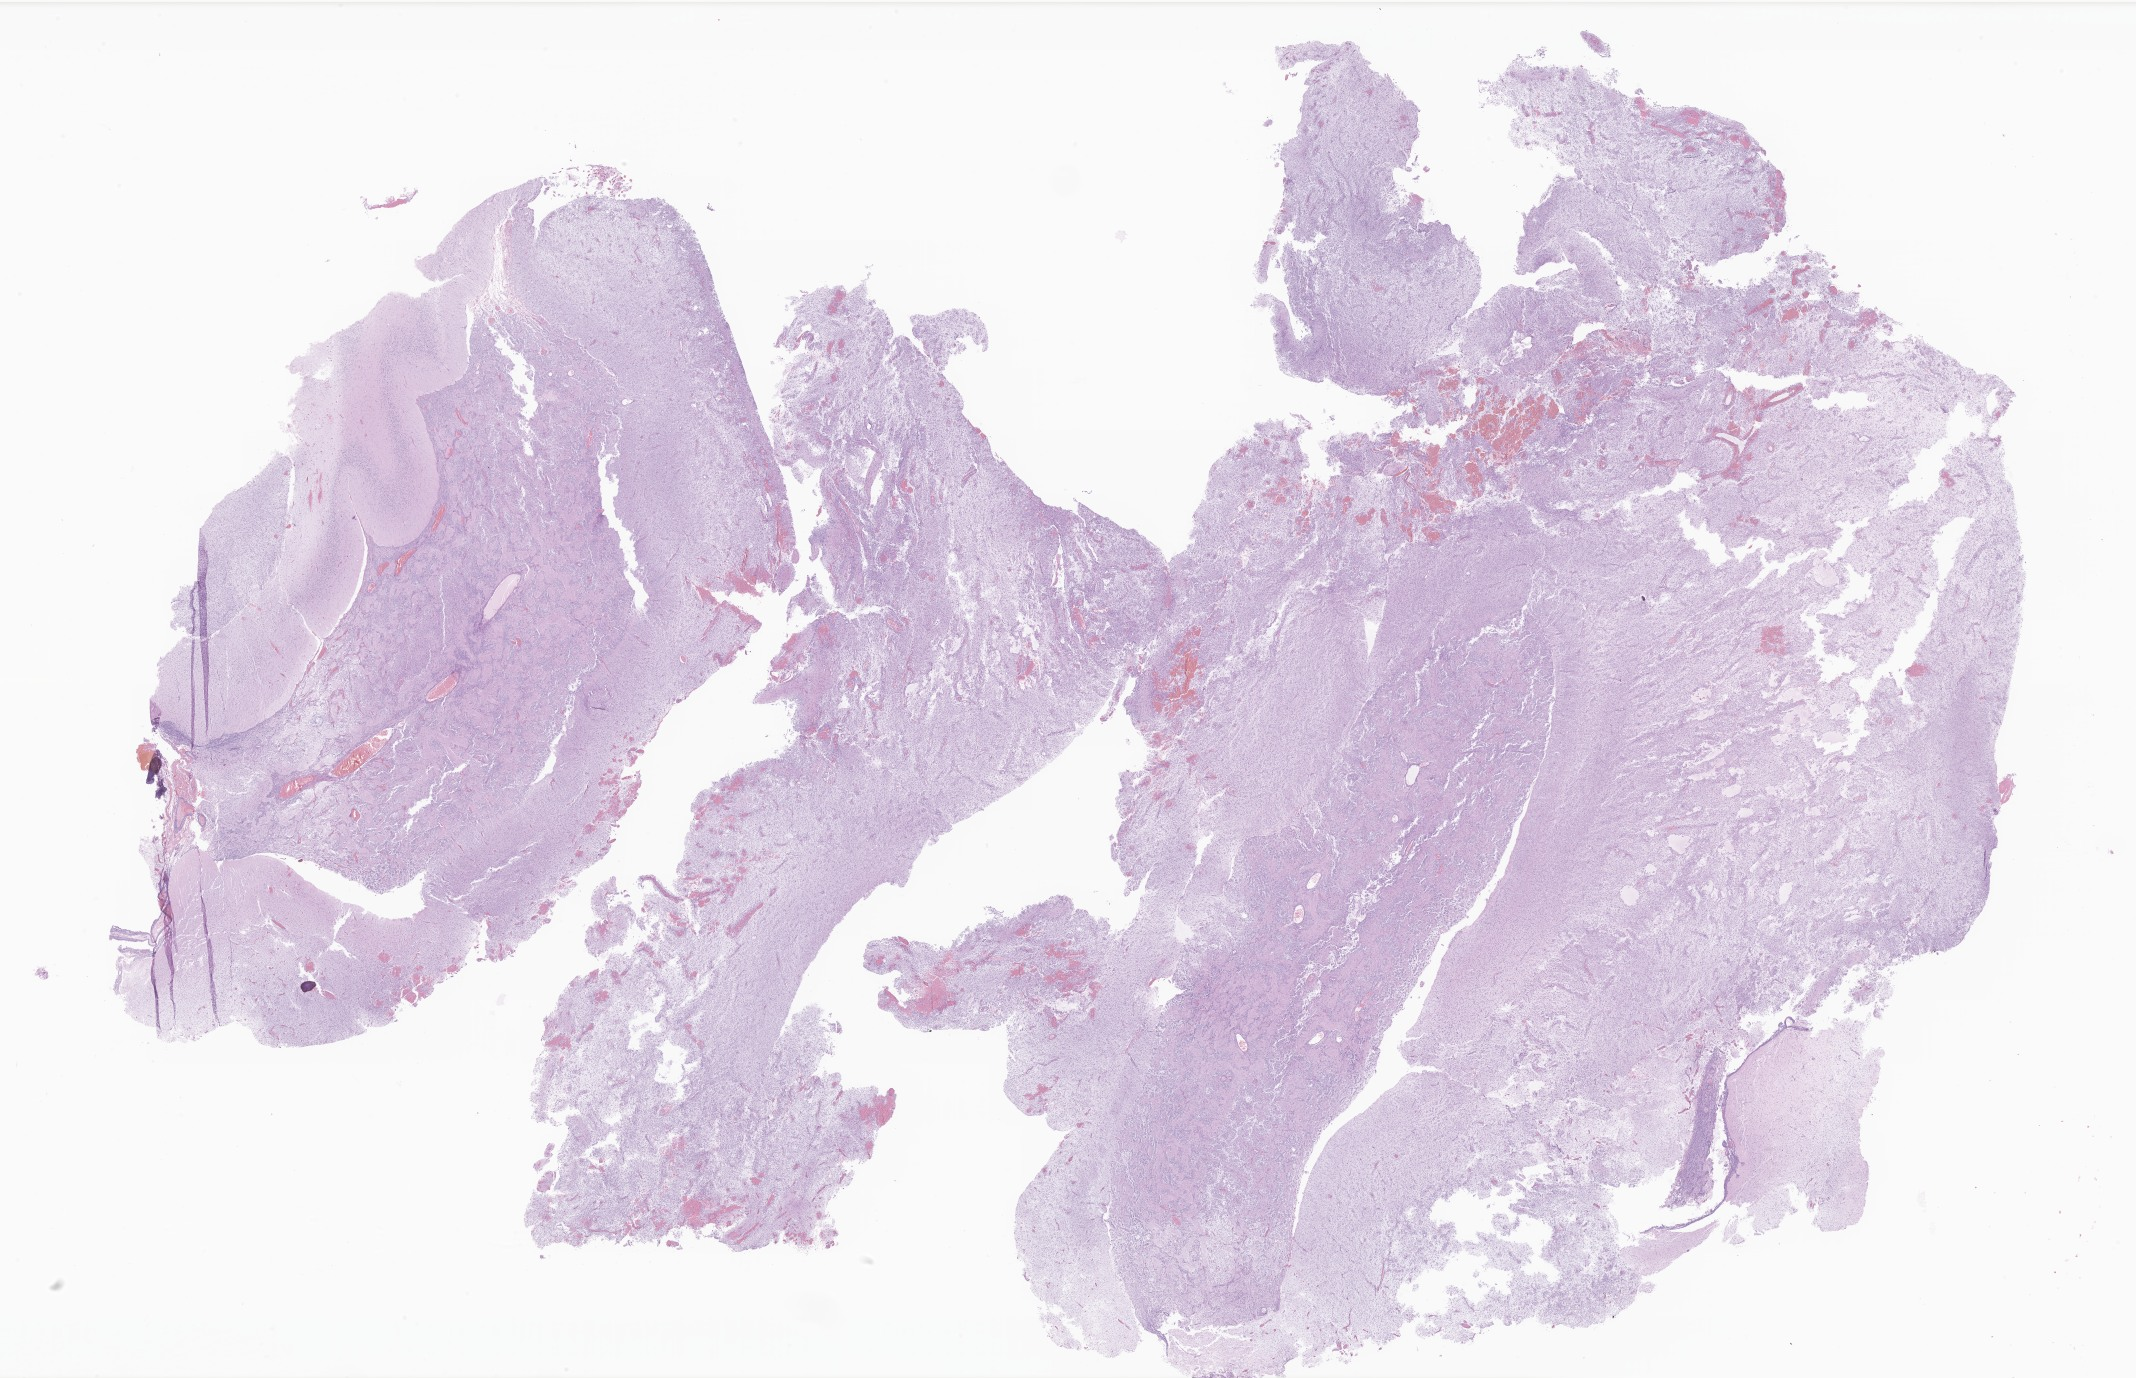
Whole-slide image, H&E stain of tumor tissue from the brain, whole scanned area (about 36.0 x 23.2 mm) shown as a low-resolution overview. Formalin-fixed, paraffin-embedded (FFPE) tissue. Patient female; age 689 days (about 1.9 years).
• diagnosis (ICD-O-3 morphology term): Pilocytic astrocytoma